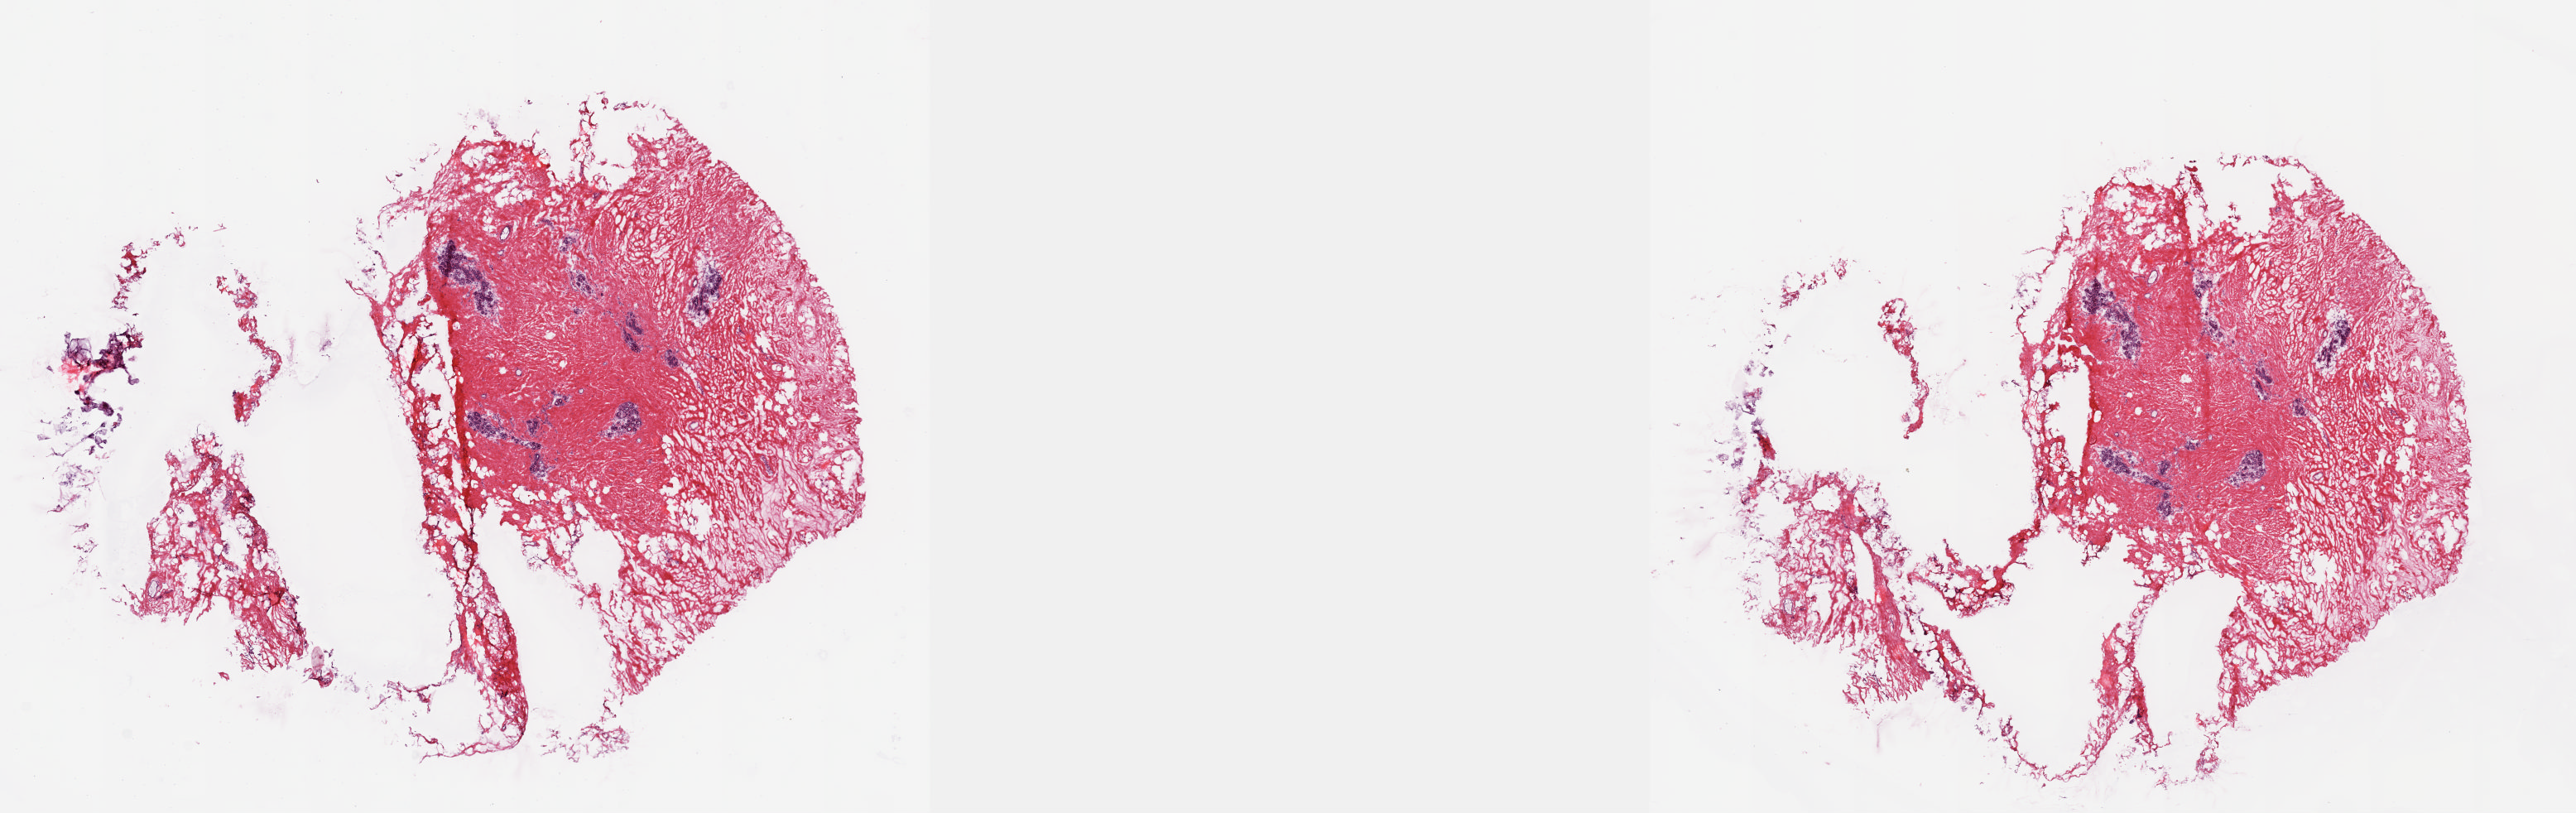
H&E-stained whole-slide image — low-resolution overview of the scanned area, about 25.1 x 7.9 mm (slide scanned at 20x); frozen section; breast, solid tissue normal (non-tumour tissue) sample. Patient: female, age at initial diagnosis 46 years.
This section: solid tissue normal (non-tumour) sample from the same patient. Patient diagnosis: Lobular carcinoma, NOS.